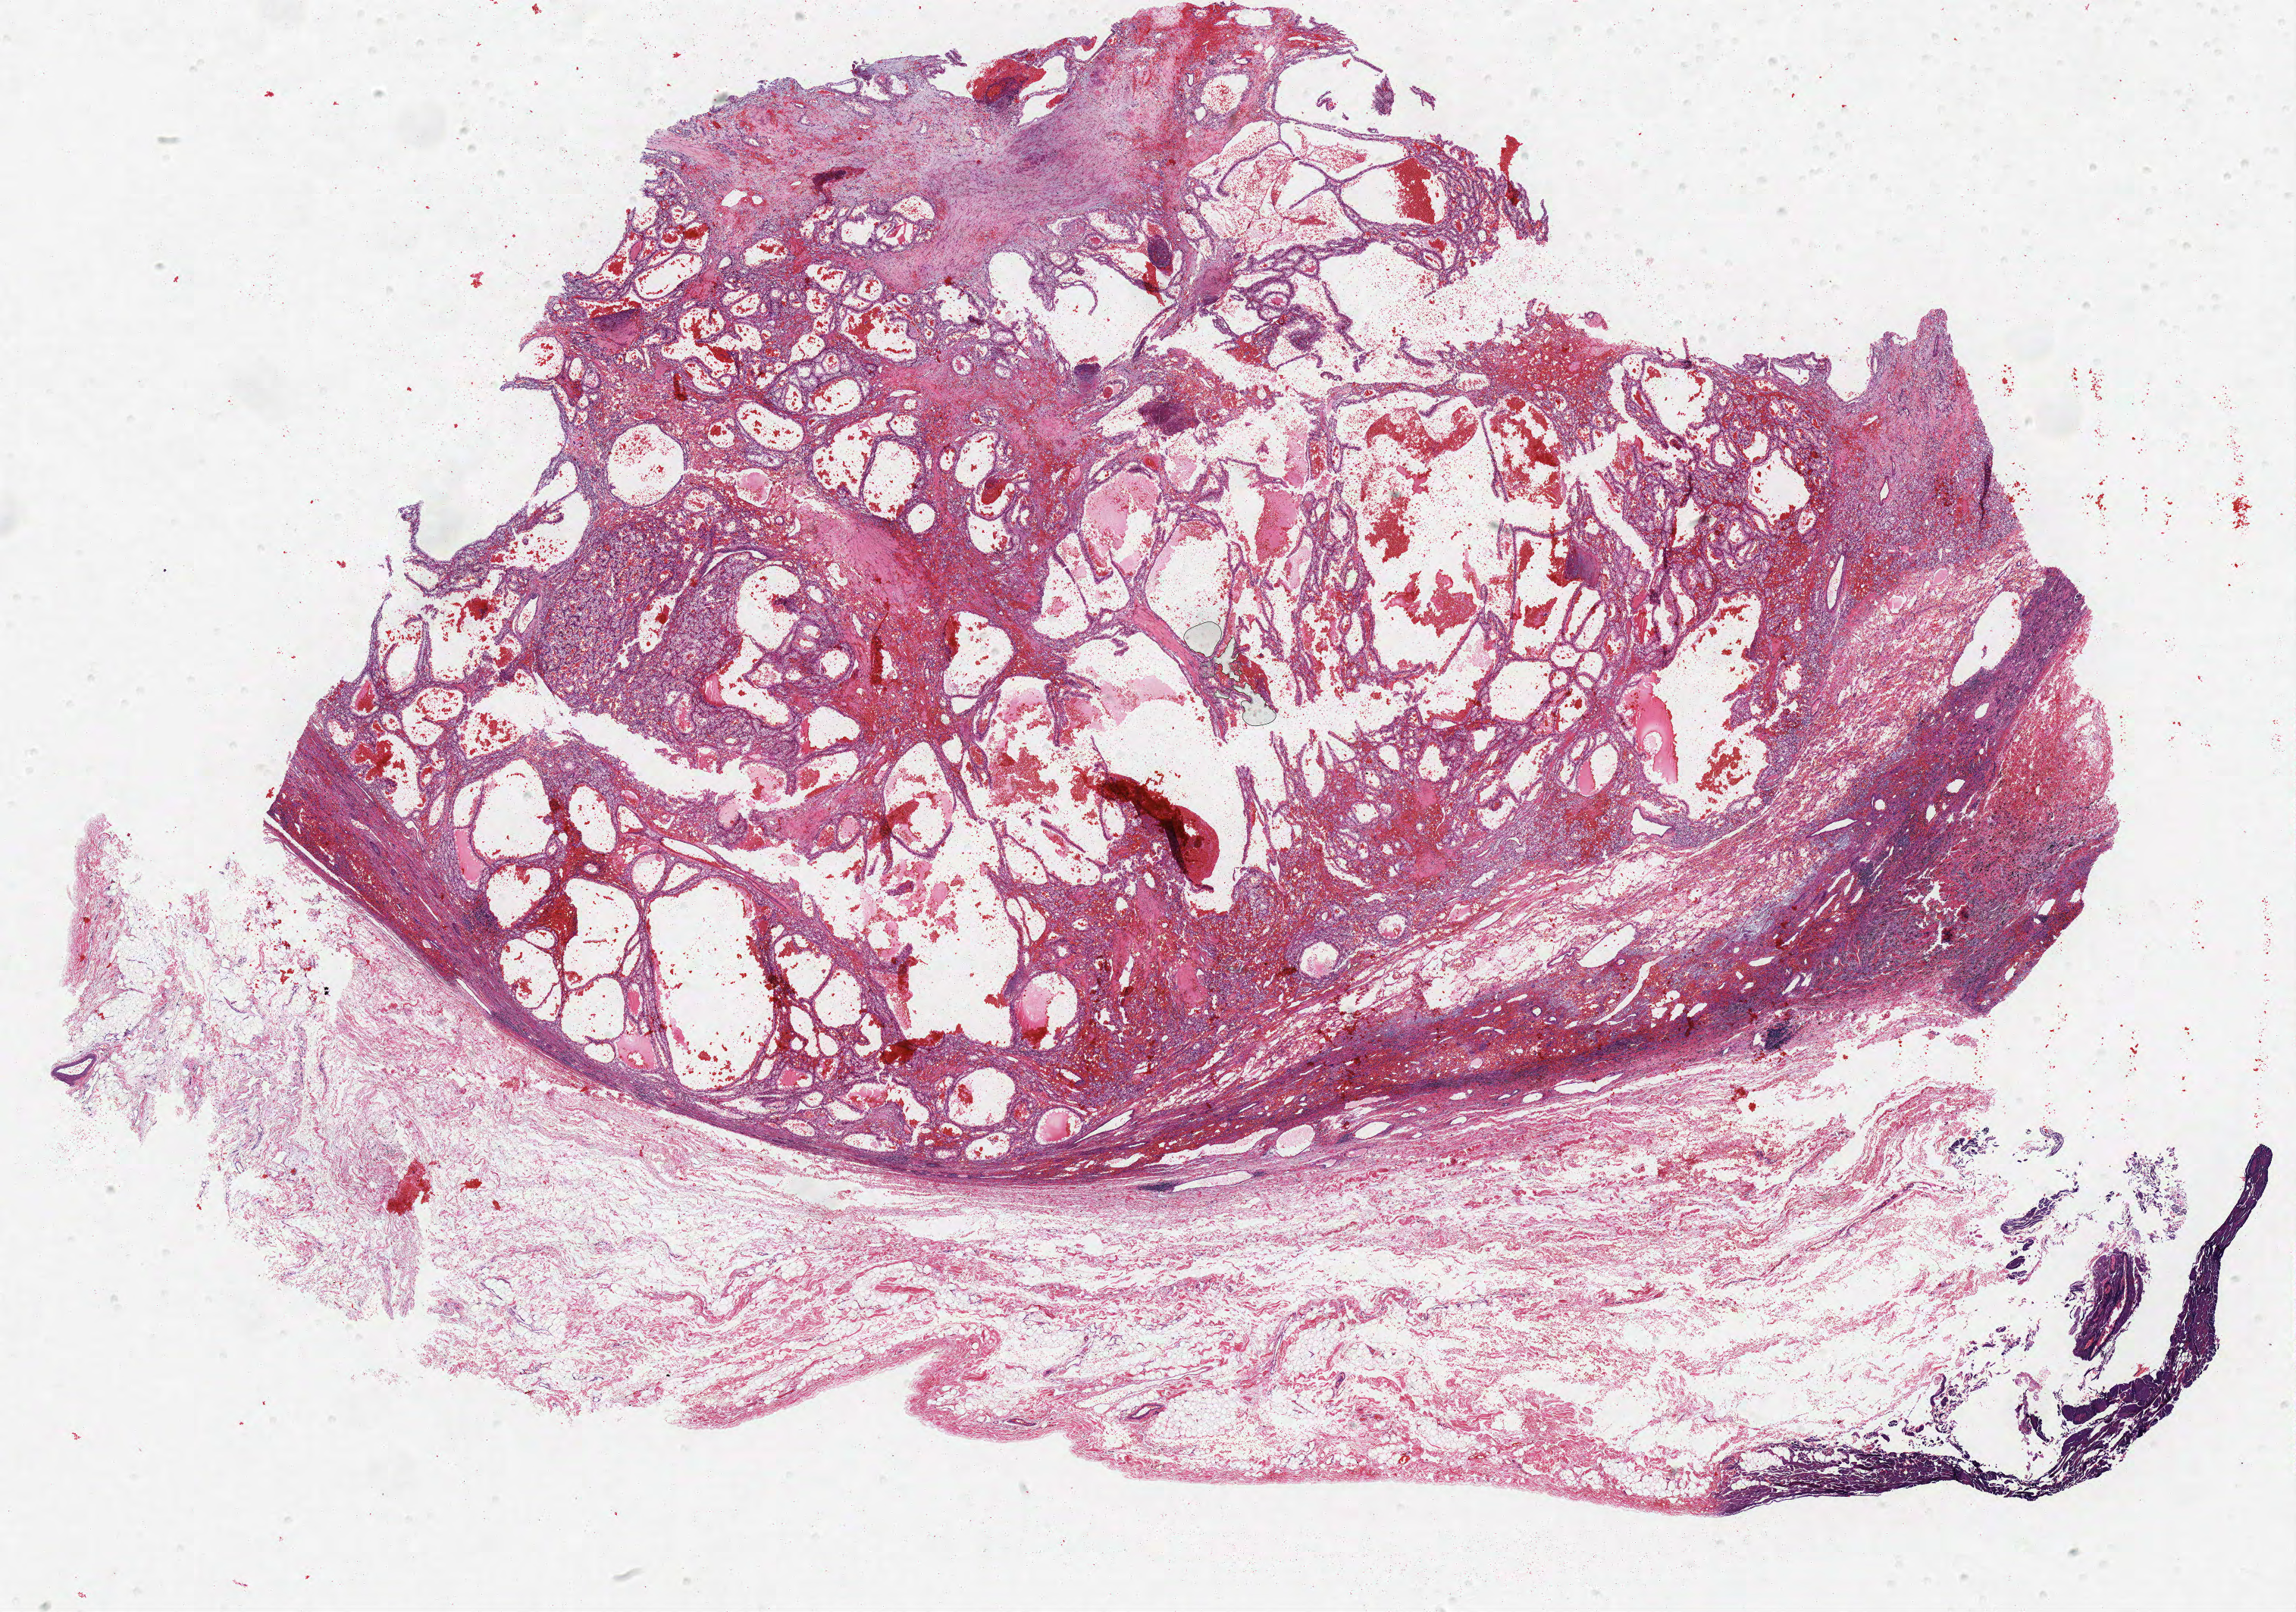
Digitized Hematoxylin and eosin (H&E) stained tissue section (whole slide), a low-resolution overview of the entire scanned area, about 24.2 x 17.0 mm (slide scanned at 40x), formalin-fixed paraffin-embedded (FFPE) diagnostic section, sample: primary tumour, kidney. Patient: male, age at initial diagnosis 54 years. Histologic grade: G2 (moderately differentiated).
• laterality: right
• AJCC pathologic stage: I
• TNM: T1a NX M0
• diagnosis: Clear cell adenocarcinoma, NOS